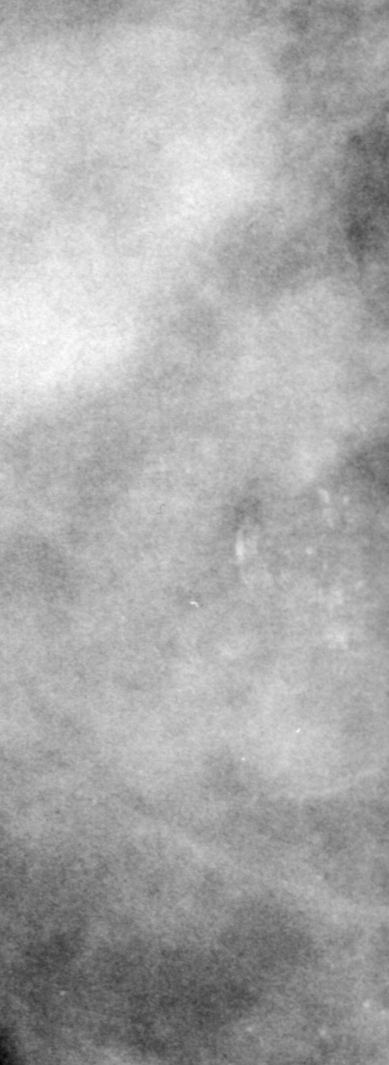
Crop from a digitized film mammogram around one marked abnormality, right breast, CC view, BI-RADS breast density category 4 (scale 1–4).
Marked abnormality: calcifications, morphology pleomorphic, distribution segmental; BI-RADS assessment category 5; pathology (as recorded): malignant.